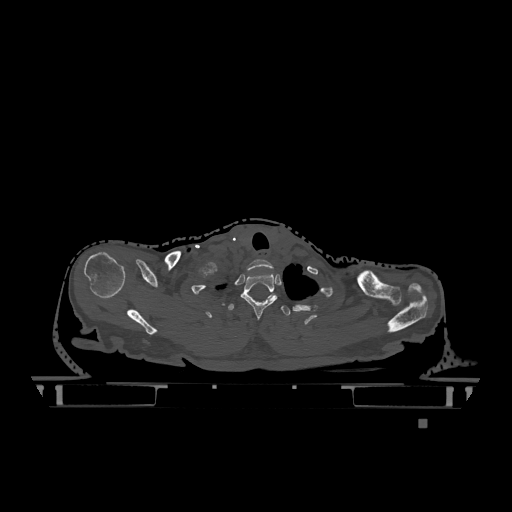
CT including the spine, one axial slice; slice 993 of 1317 in the series (ordered by position); bone window (W 1800 / L 400 HU); 0.5 mm slice thickness; 512 × 512 image matrix. Patient: female, 74 years. From the clinical record (not read from this slice): primary cancer: lung; vertebrae with lytic lesions (as recorded): T1, T4, T5, T6, L4, L5.
Annotated regions visible in this slice (semi-automatic segmentation, software-assisted and operator-edited):
- T1 vertebra: bounding box (x1, y1, x2, y2) in pixels: (241, 273, 278, 319)
- T2 vertebra: (228, 295, 291, 316)